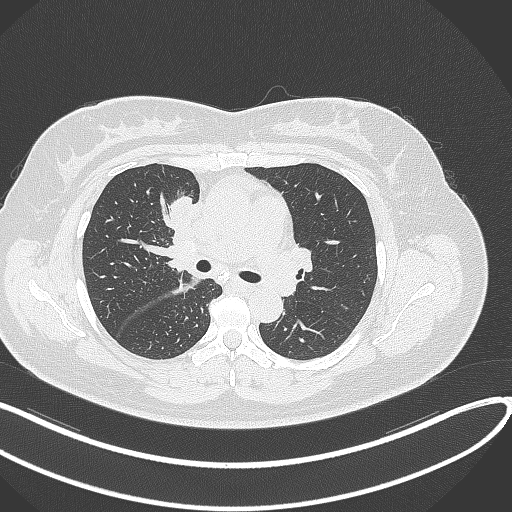
Chest CT, one axial slice. Position 168 of 303 along the scan axis. Reconstruction kernel B70f. 120 kVp. Lung window (W 1500 / L -600 HU). 1 mm slice thickness. 512 × 512 image matrix, field of view 400 × 400 mm. Patient: female, 46 years. Case-level facts recorded for this patient, not image findings: clinical TNM (as recorded): T2a N1 M0.
Annotated regions visible in this slice (rectangle marked by the reading radiologist):
- lung tumour (recorded histology: adenocarcinoma): bounding box [x1, y1, x2, y2] px = [166, 193, 198, 239]